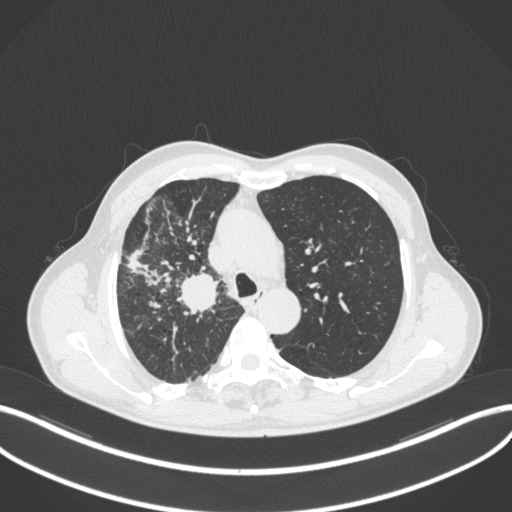
Chest CT, one axial slice; slice 345 of 490 in the series (ordered by position); reconstruction kernel B31f; lung window (W 1500 / L -600 HU); 512 × 512 image matrix, field of view 400 × 400 mm. Patient: male, 69 years. Case-level facts recorded for this patient, not image findings: clinical TNM (as recorded): T2a N0 M0.
Structures marked on this image (rectangle marked by the reading radiologist):
- lung tumour (recorded histology: adenocarcinoma): bounding box <173,271,221,314> (left, top, right, bottom; pixels)